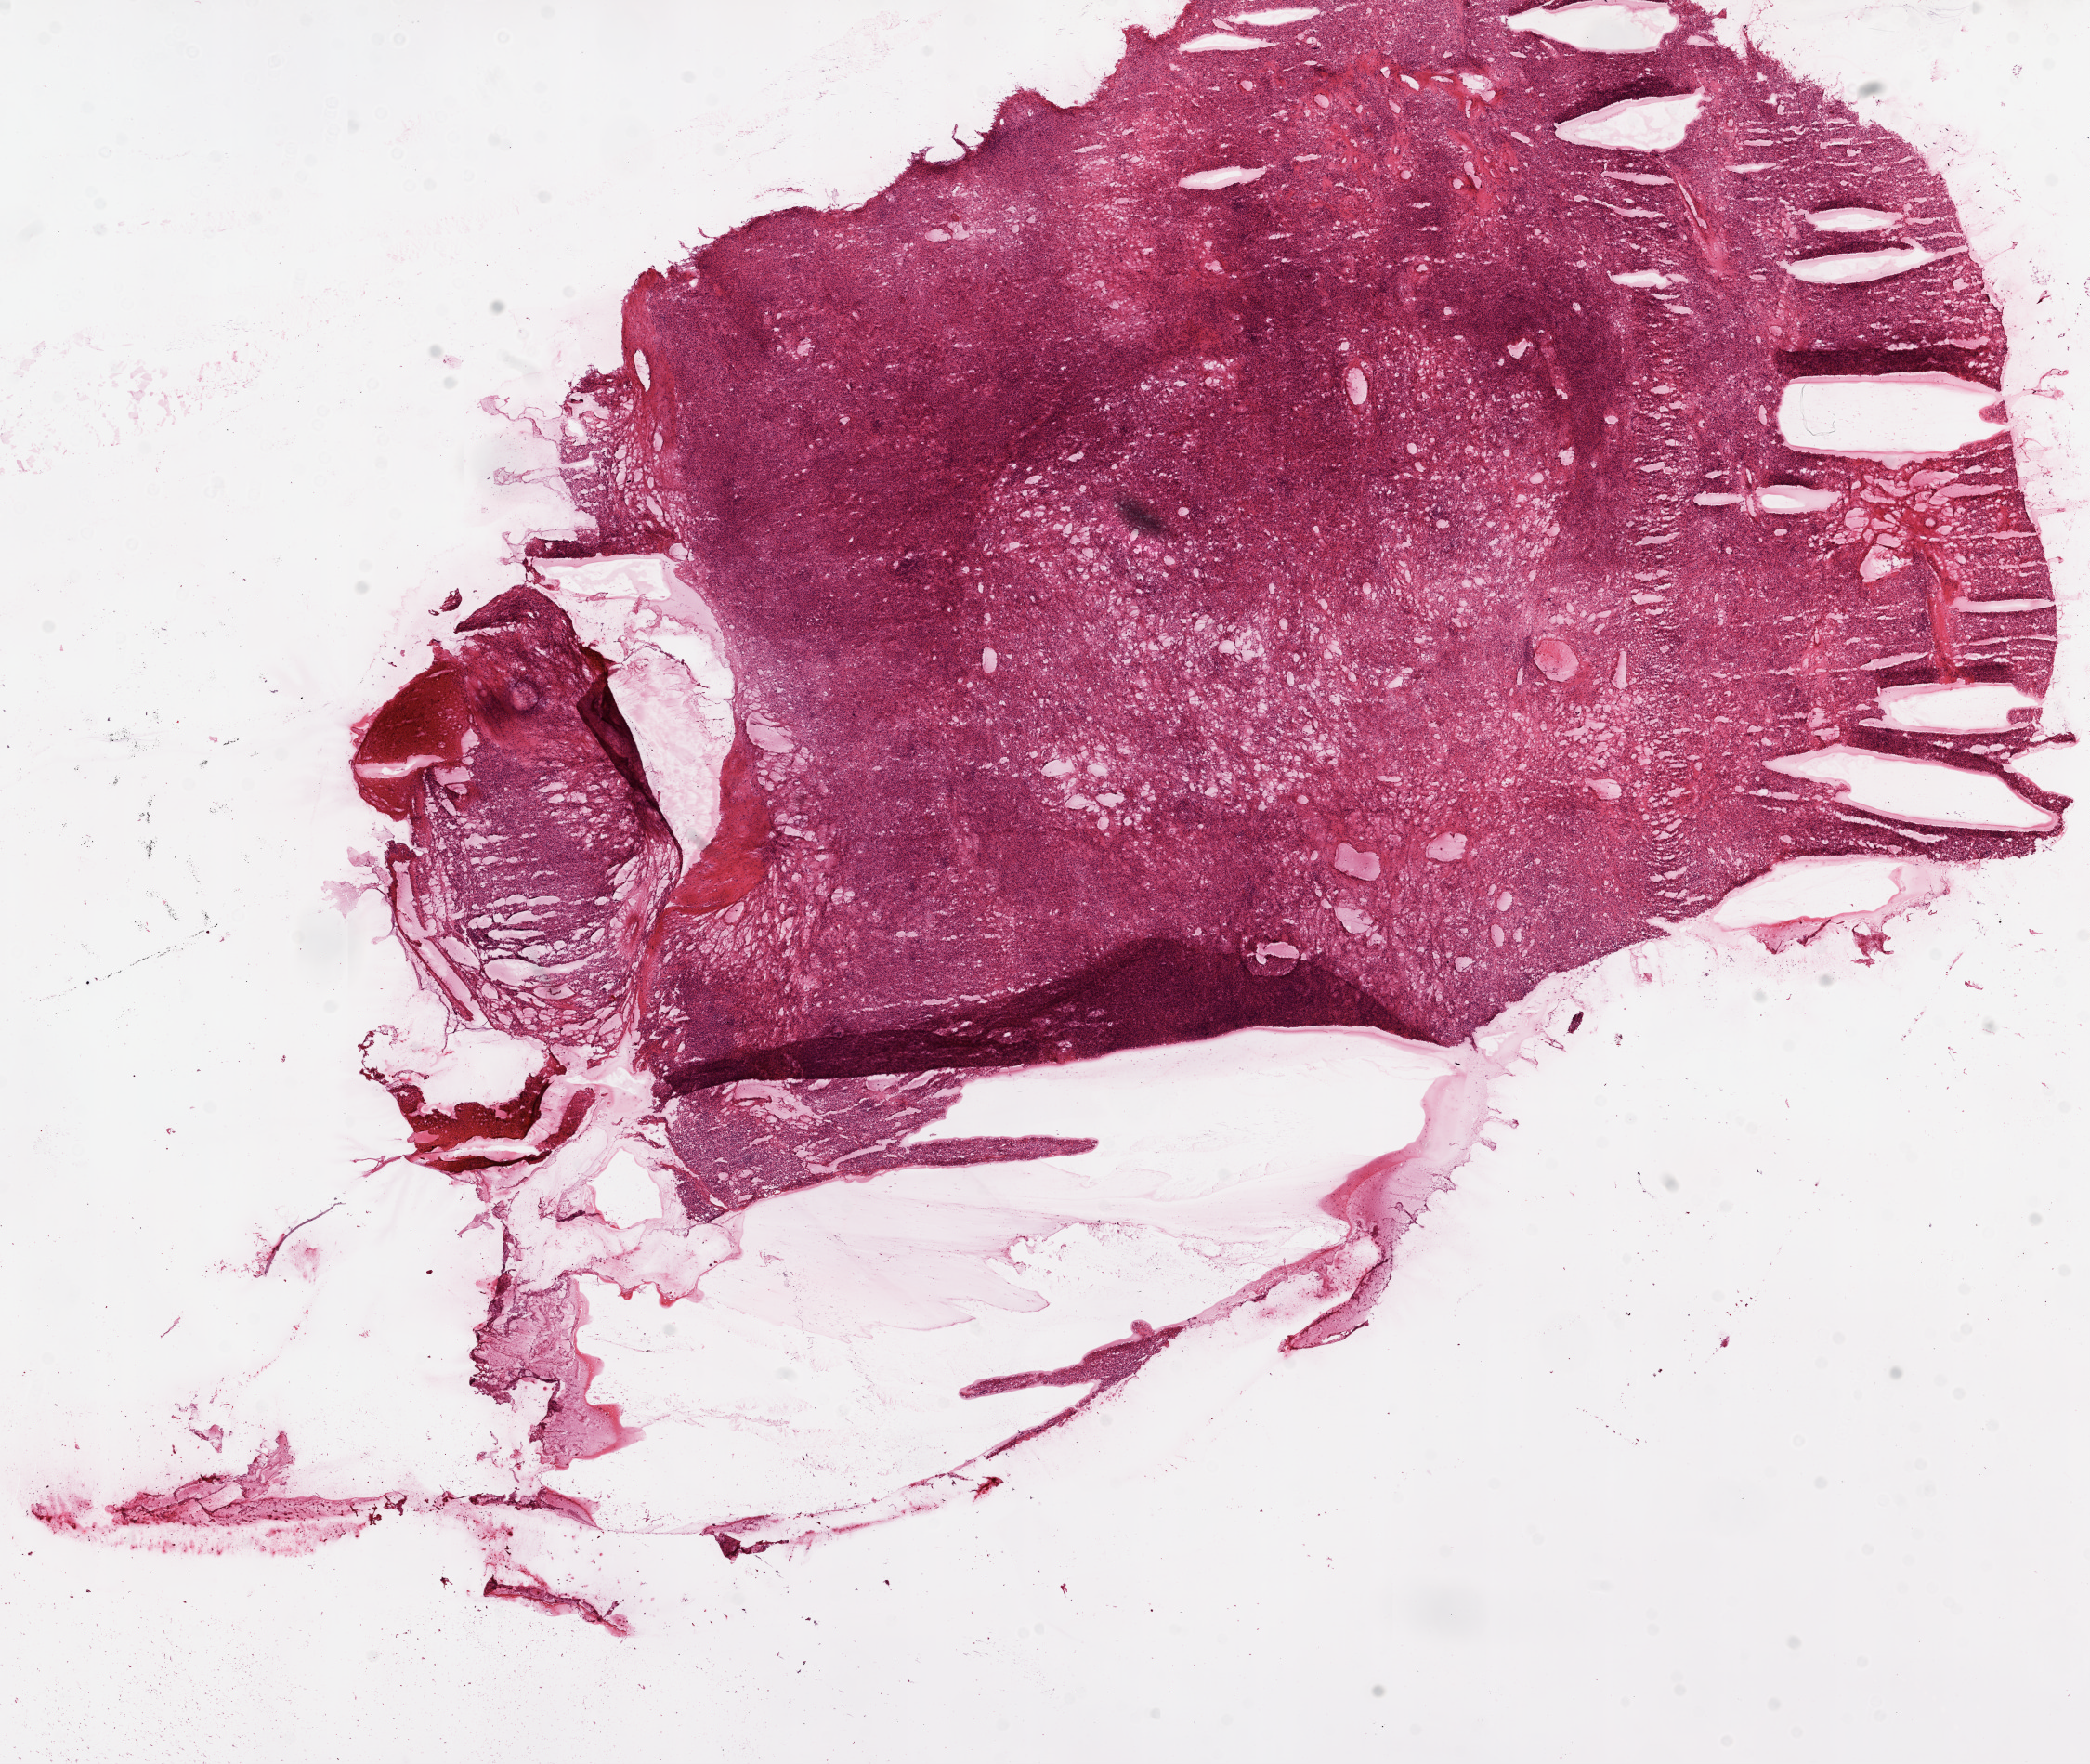
Digitized H&E tissue section (whole slide), low-resolution overview of the scanned area, about 18.1 x 15.2 mm. Frozen section from the top of the tissue portion. Kidney, primary tumour sample. Female, age 68 years at initial diagnosis. Slide review estimates, as recorded: tumour cells 90%, tumour nuclei 90%.
Histologic diagnosis: Clear cell adenocarcinoma, NOS.